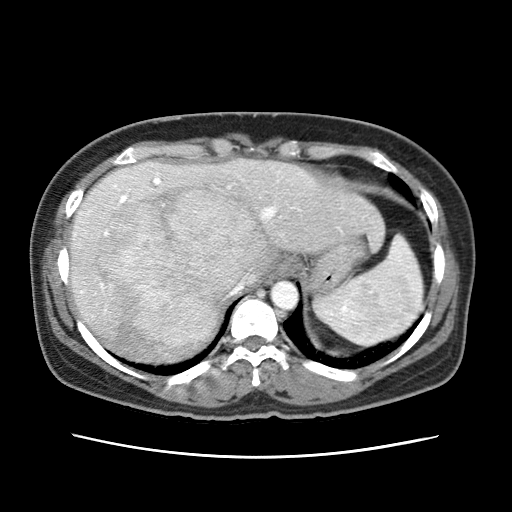
Contrast-enhanced abdominal CT (liver protocol), one axial slice; slice 53 of 79 in the series (ordered by position); reconstruction kernel STANDARD; soft-tissue window (W 400 / L 40 HU); 2.5 mm slice thickness; 512 × 512 image matrix, field of view 340 × 340 mm. Case-level facts recorded for this patient, not image findings: diagnosis: hepatocellular carcinoma (patient treated with transarterial chemoembolisation; whether this scan precedes or follows treatment is not stated here); TNM stage (as recorded): Stage-I; Child-Pugh class: A.
Structures marked on this image (semi-automatically segmented with operator editing):
- abdominal aorta: bounding box (x1, y1, x2, y2) in pixels: (272, 281, 298, 310)
- liver parenchyma outside the tumour (the mass and vessels are separate outlines, so this box may not span the whole liver): (68, 158, 382, 360)
- mass: (99, 179, 266, 345)
- liver vessels: (75, 173, 275, 294)